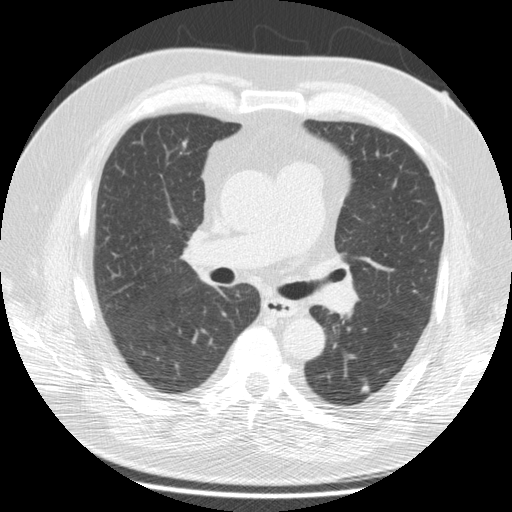
Low-dose screening chest CT, one axial slice. Slice 102 of 172 in the series (ordered by position). Lung window (W 1500 / L -600 HU). 2.5 mm slice thickness. 512 × 512 image matrix.
Structures marked on this image (expert manual segmentation):
- lesion 1 (tumor, lower lobe of left lung): bounding box [x1, y1, x2, y2] px = [361, 385, 370, 394]